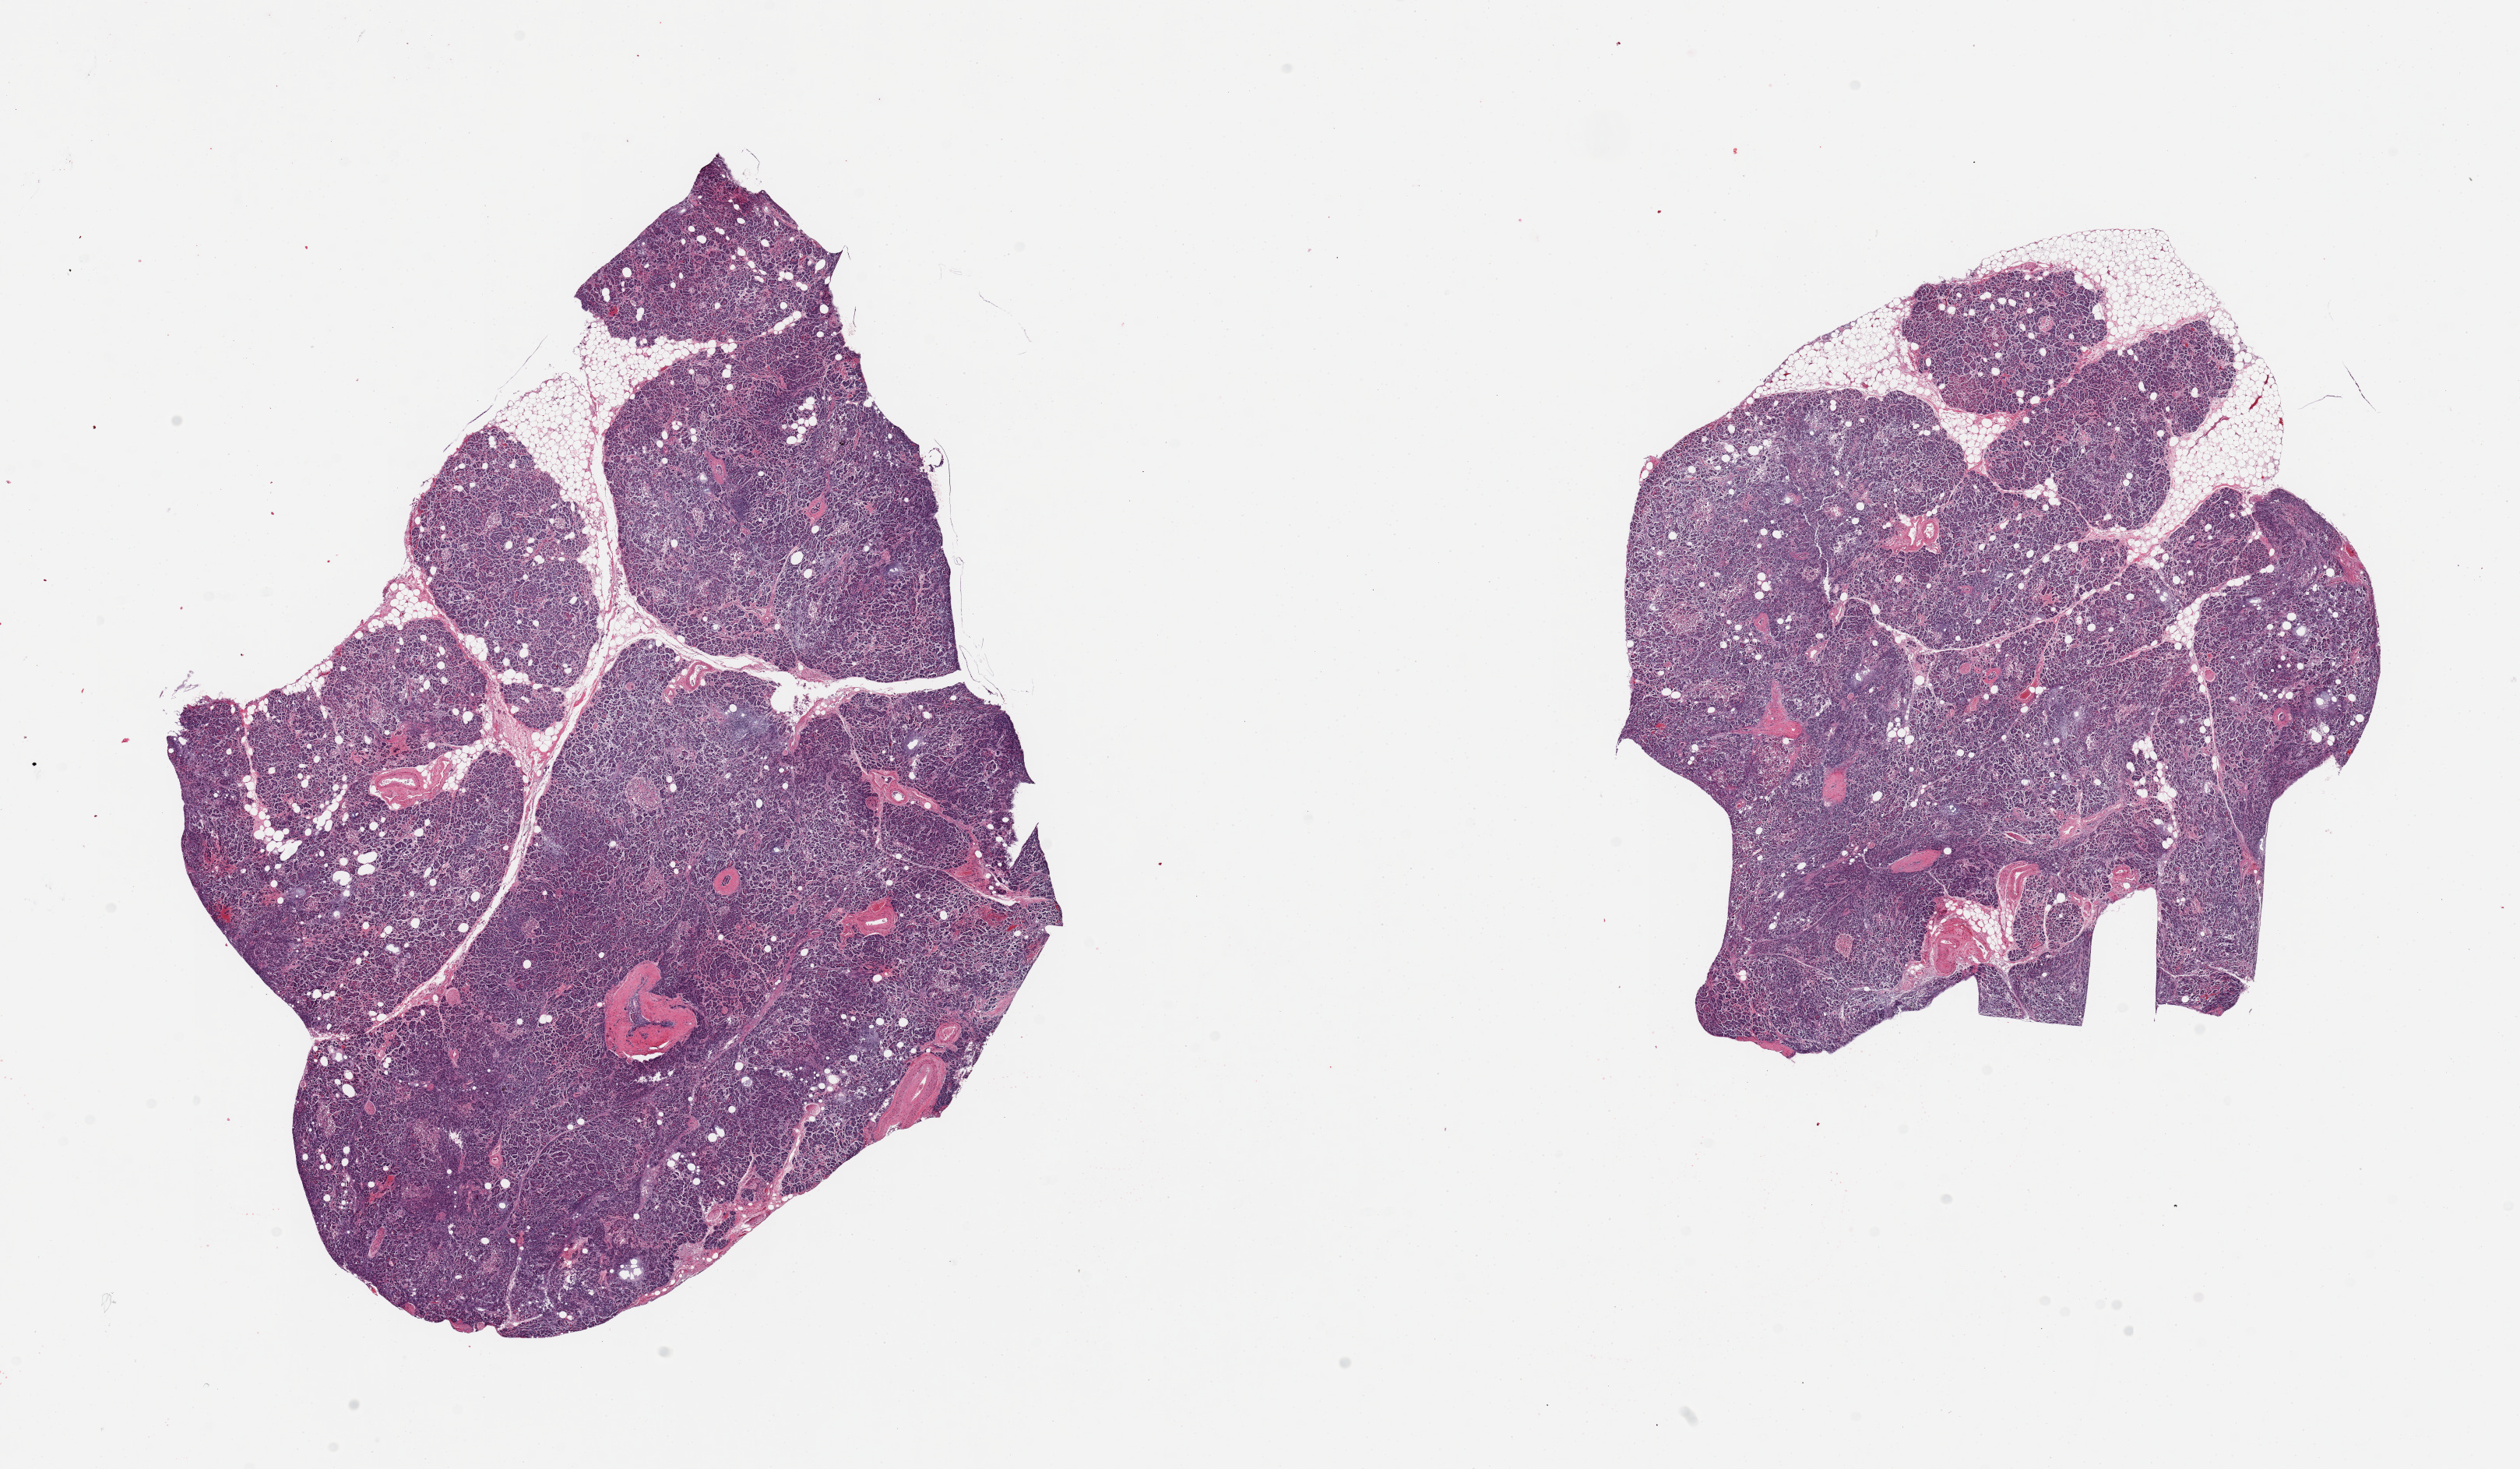
H&E whole-slide image, low-resolution overview of the scanned area, about 25.6 x 14.9 mm (slide scanned at 20x), PAXgene-fixed, paraffin-embedded tissue, section of pancreas (target tissue), tissue donor sample. Donor sex: male.
Reviewer comment on this tissue sample: 2 pieces; 10% internal and external fat.